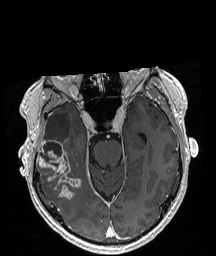
Brain MRI from a brain-tumour surgery series, one axial slice. Slice 128 of 208 in the series (ordered by position). T1-weighted post-contrast. 216 × 256 image matrix, field of view 211 × 250 mm. Case-level facts recorded for this patient, not image findings: histopathology: Astrocytoma; WHO grade: 4; IDH mutation: yes; tumour location: Right Temporal.
Outlined on this slice (expert manual segmentation):
- tumour: box from (x=37, y=139) to (x=81, y=199) px